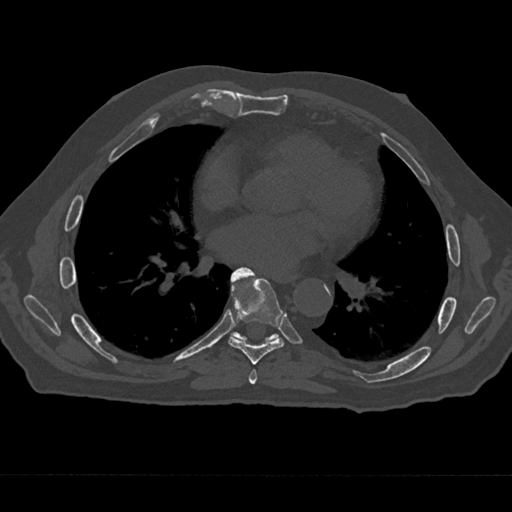
CT including the spine, one axial slice; position 357 of 797 along the scan axis; reconstruction kernel Br40s/3; bone window (W 1800 / L 400 HU); 0.5 mm slice thickness; 512 × 512 image matrix. Patient: male, 75 years. Case-level facts recorded for this patient, not image findings: primary cancer: renal.
Annotated regions visible in this slice (semi-automatically segmented with operator editing):
- T6 vertebra: bounding box <249,369,258,385> (left, top, right, bottom; pixels)
- T7 vertebra: <228,267,284,365>
- T8 vertebra: <230,332,279,342>